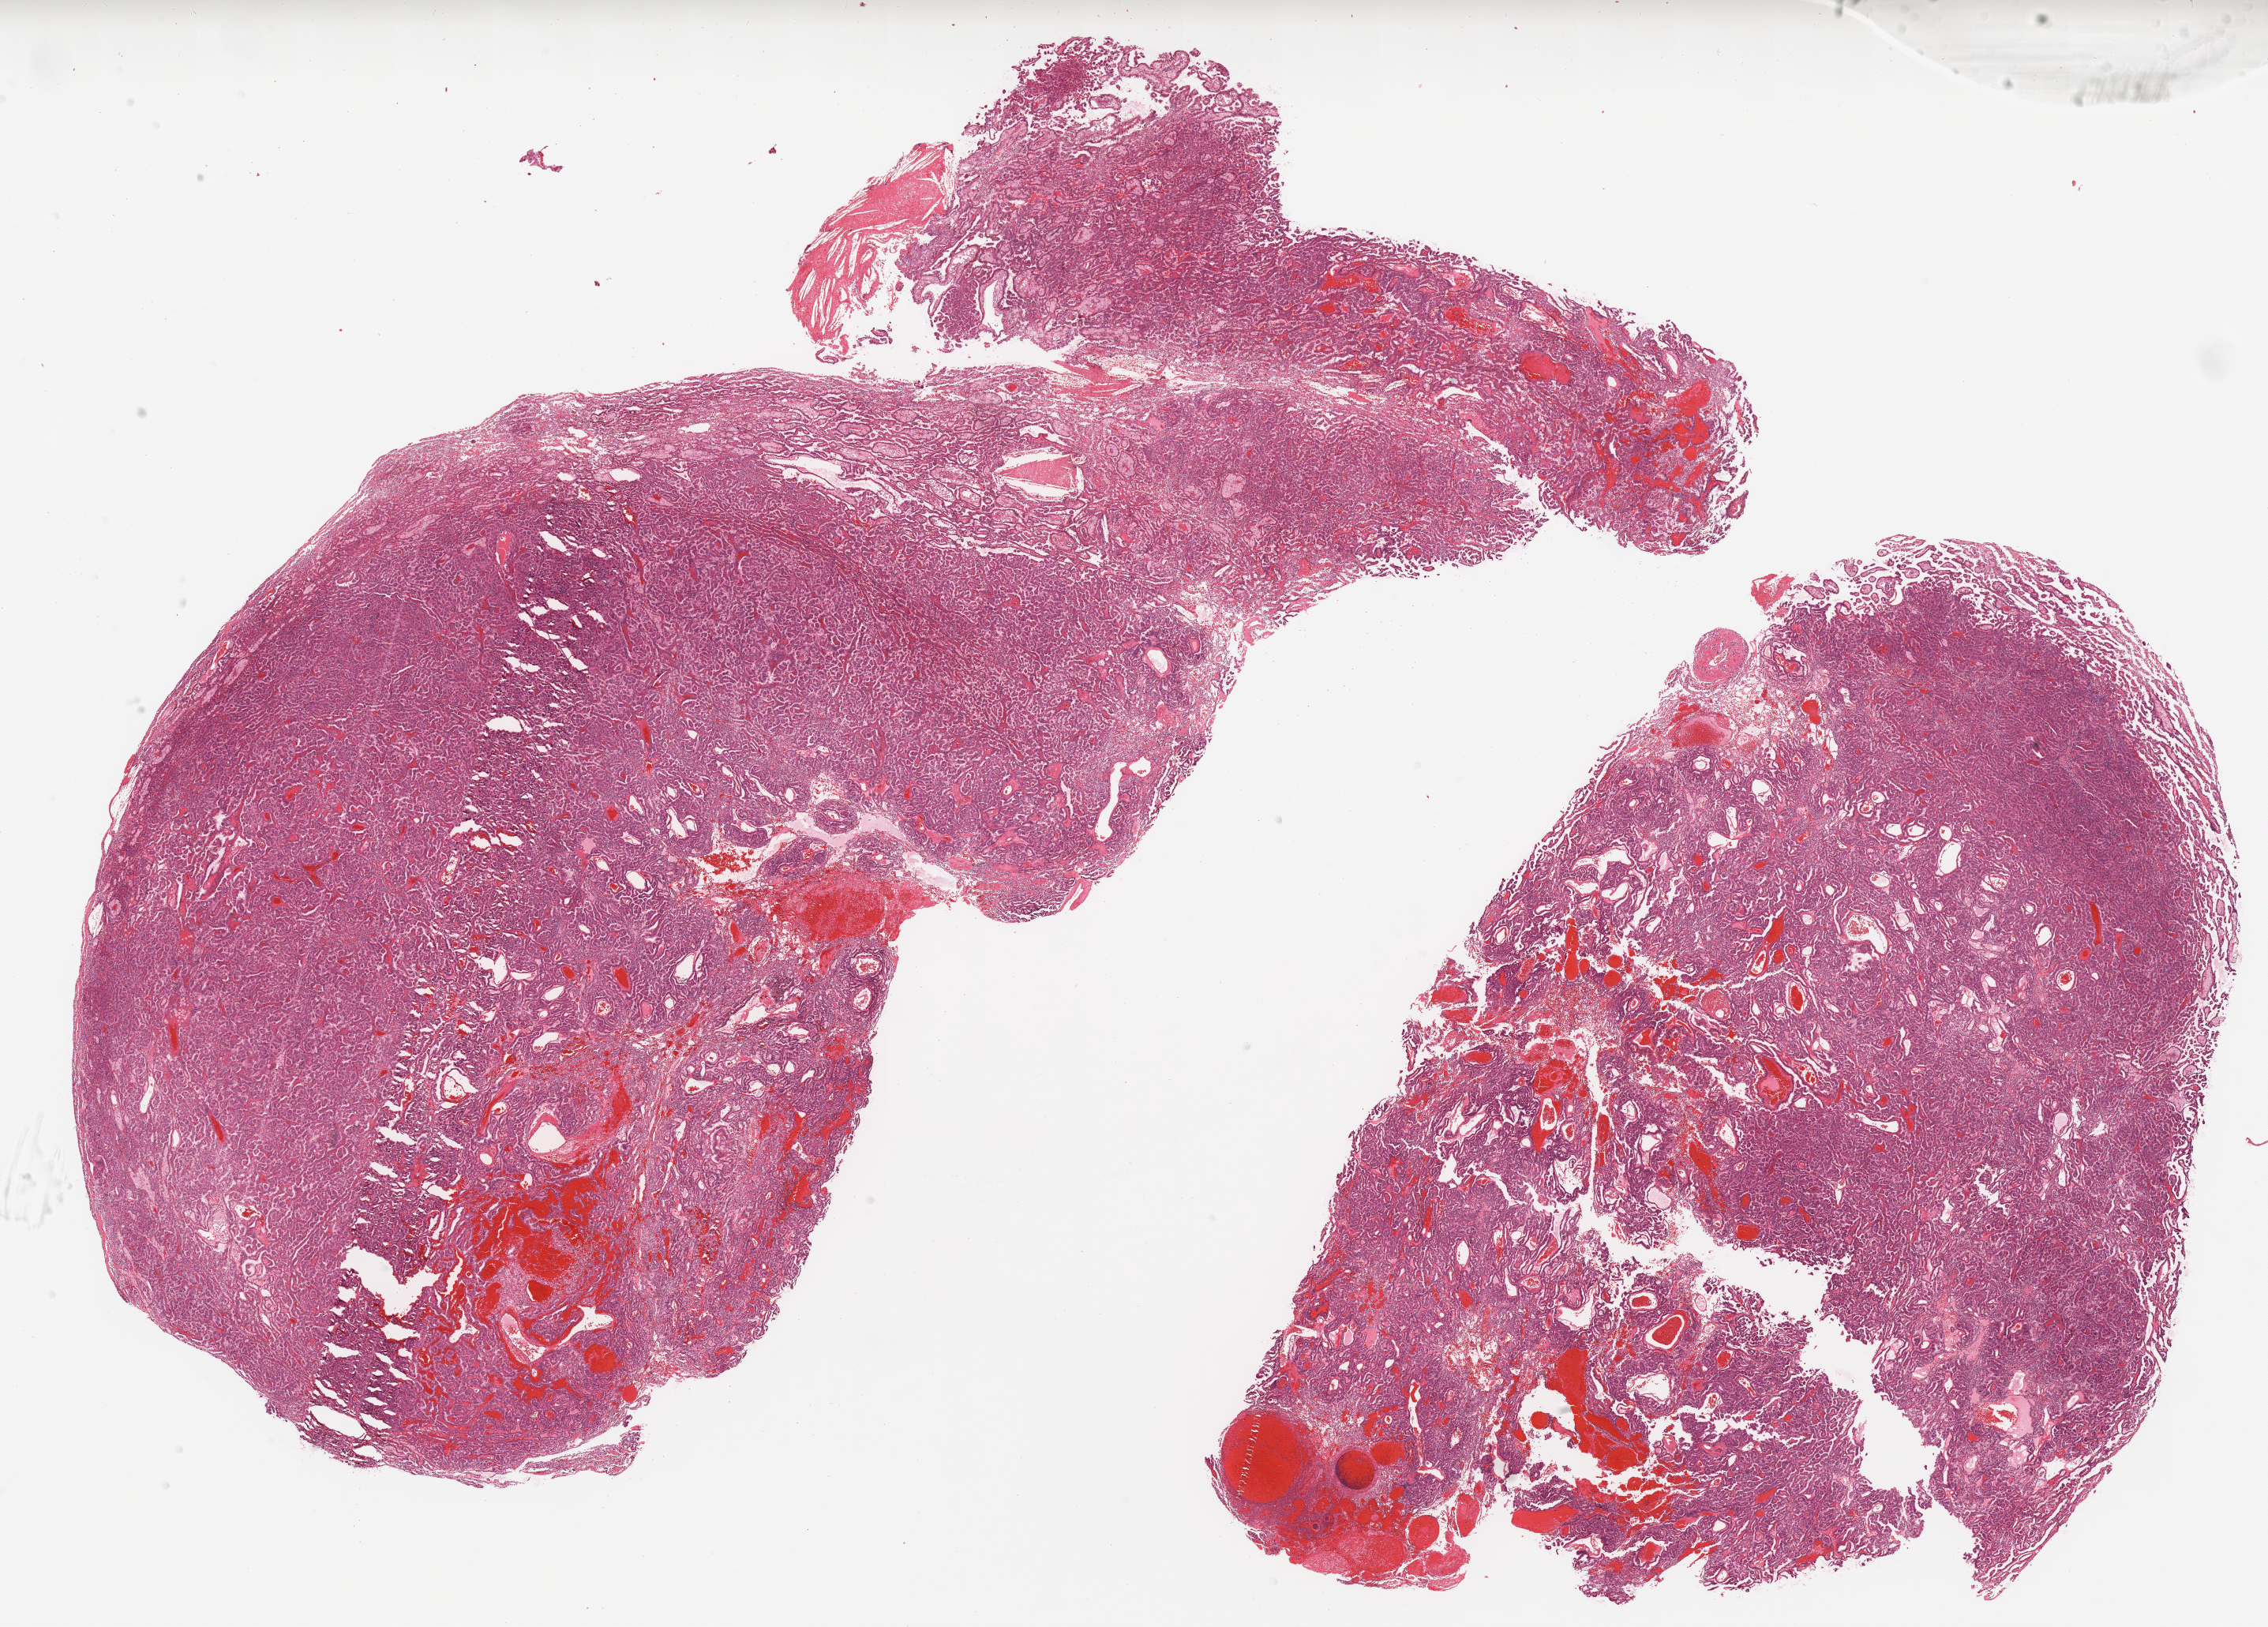
H&E-stained whole-slide image — whole scanned area (about 23.0 x 16.5 mm) shown as a low-resolution overview. Formalin-fixed paraffin-embedded (FFPE) diagnostic section. Sample: primary tumour, kidney. Male patient.
AJCC pathologic stage: II (6th edition). Histologic diagnosis: Papillary adenocarcinoma, NOS.